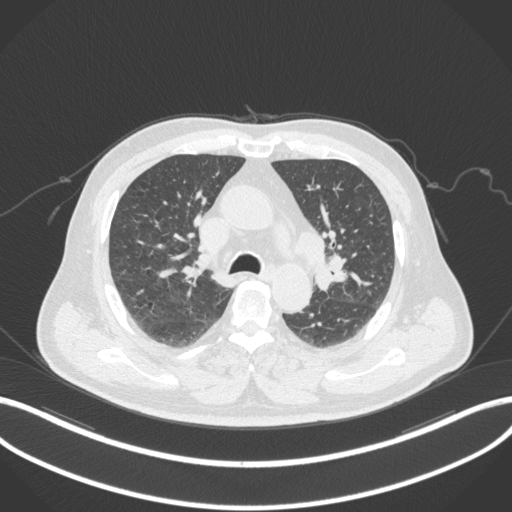
Chest CT, one axial slice; position 196 of 286 along the scan axis; 120 kVp; lung window (W 1500 / L -600 HU); 1 mm slice thickness; 512 × 512 image matrix, field of view 400 × 400 mm. Patient: male, 67 years. Case-level facts recorded for this patient, not image findings: clinical TNM (as recorded): T2a N1 M0; histopathological grade: G3.
Annotated regions visible in this slice (bounding box drawn by a radiologist):
- lung tumour (recorded histology: adenocarcinoma): bounding box [x1, y1, x2, y2] px = [313, 250, 348, 293]